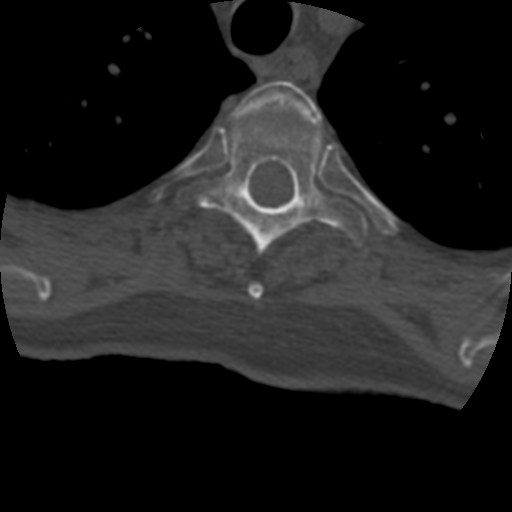
CT including the spine, one axial slice; slice 339 of 399 in the series (ordered by position); reconstruction kernel STANDARD; 120 kVp; bone window (W 1800 / L 400 HU); 1.25 mm slice thickness; 512 × 512 image matrix, field of view 160 × 160 mm. Patient age 69 years. Case-level facts recorded for this patient, not image findings: primary cancer: prostate.
Annotated regions visible in this slice (semi-automatically segmented with operator editing):
- T3 vertebra: bounding box <236,80,321,299> (left, top, right, bottom; pixels)
- T4 vertebra: <175,113,369,256>